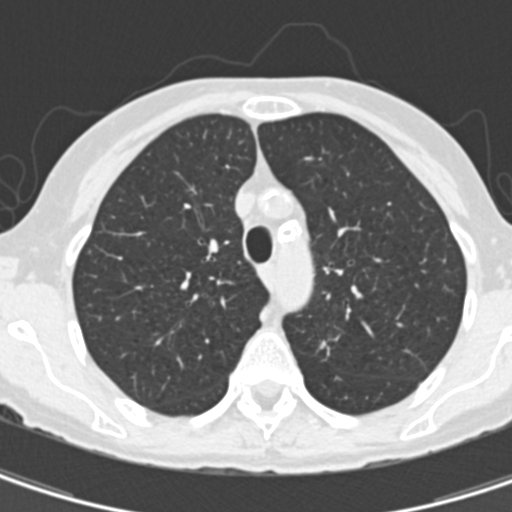
Low-dose screening chest CT, axial slice. Baseline screening round. Lung window (W 1500 / L -600 HU). Standard (soft-tissue) reconstruction kernel (B30f). Slice 44 of 157 in the series. 512 × 512 image matrix, field of view 260 × 260 mm. Female, age 67 years at enrolment. Current smoker at enrolment.
Expert-annotated lung lesion, box from (x=307, y=322) to (x=348, y=376) px. Reader record for this screening exam (exam-level; its link to the box is not recorded): non-calcified nodule or mass ≥4 mm, left upper lobe, 11 × 8 mm, spiculated (stellate) margins, soft tissue attenuation. Later outcome: lung cancer diagnosed 73 days after this screen — adenocarcinoma, NOS, left upper lobe, poorly differentiated (G3), stage IA (AJCC 6th edition), 13 mm at pathology.